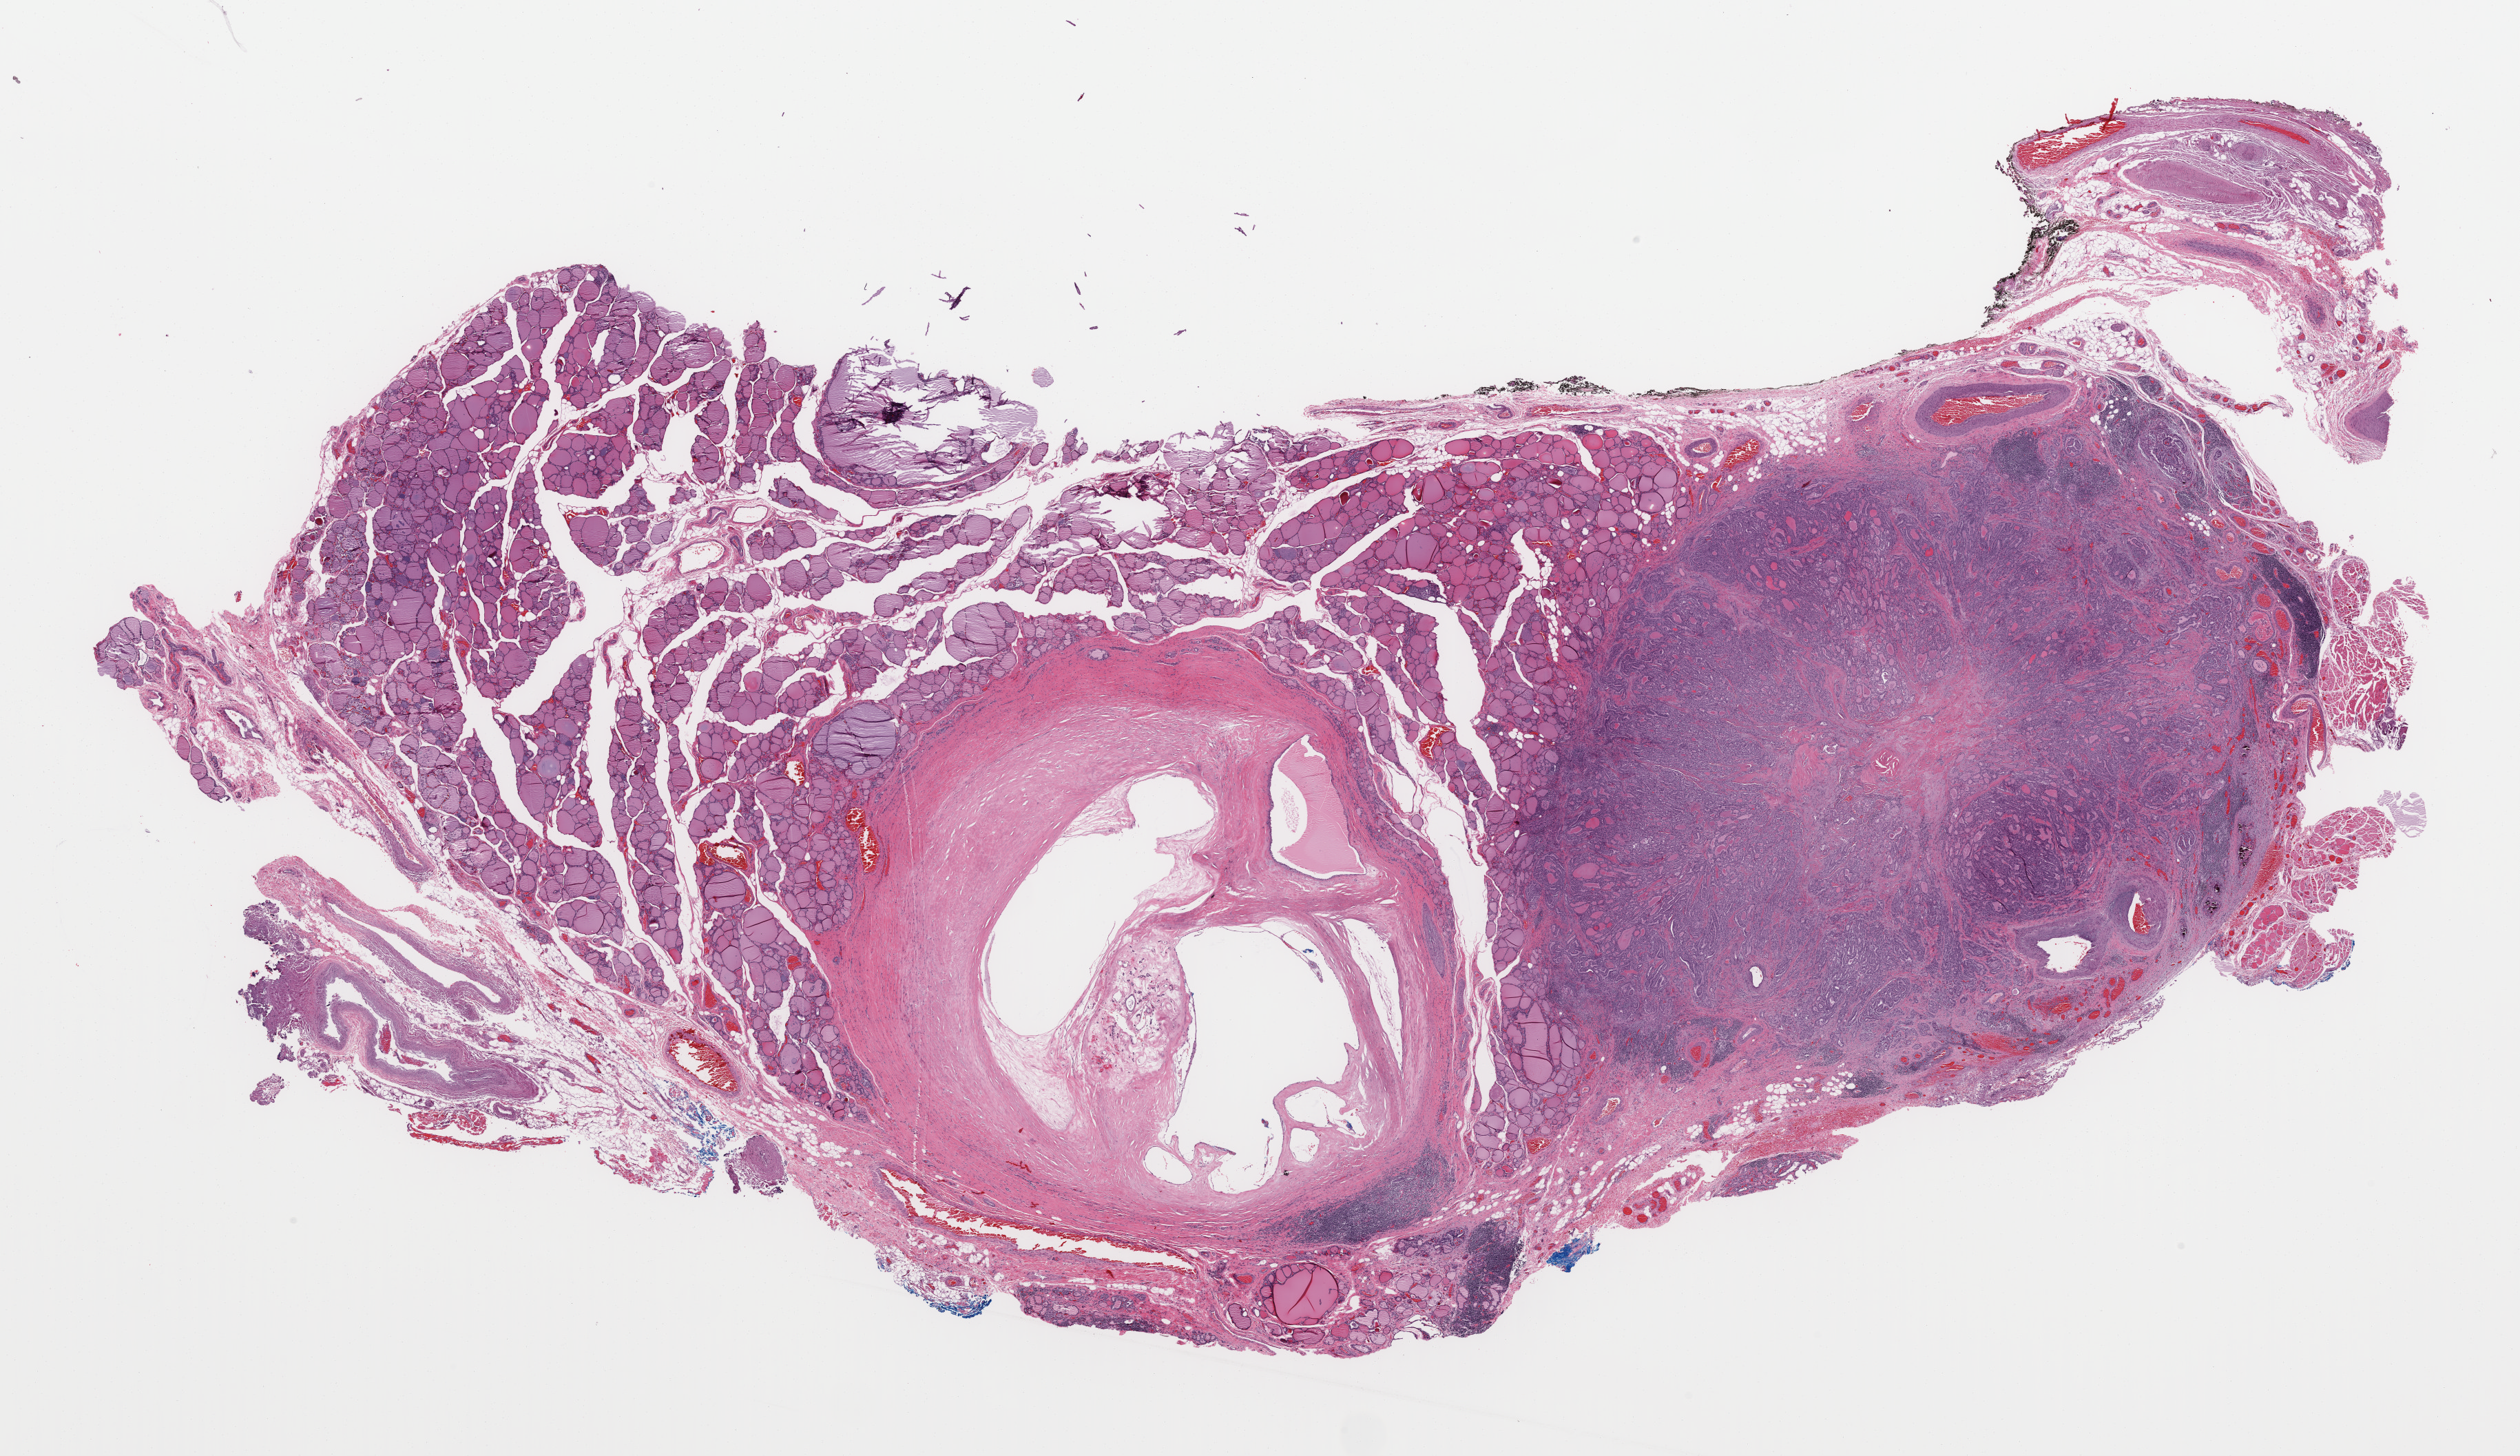
Hematoxylin and eosin (H&E) stained whole-slide image, whole scanned area (about 28.9 x 16.7 mm, acquisition: 40x scan) shown as a low-resolution overview; formalin-fixed paraffin-embedded (FFPE) diagnostic section; primary tumour sample from the thyroid. Female patient; age at initial diagnosis 60 years.
Pathologic diagnosis: Papillary carcinoma, columnar cell (thyroid gland).